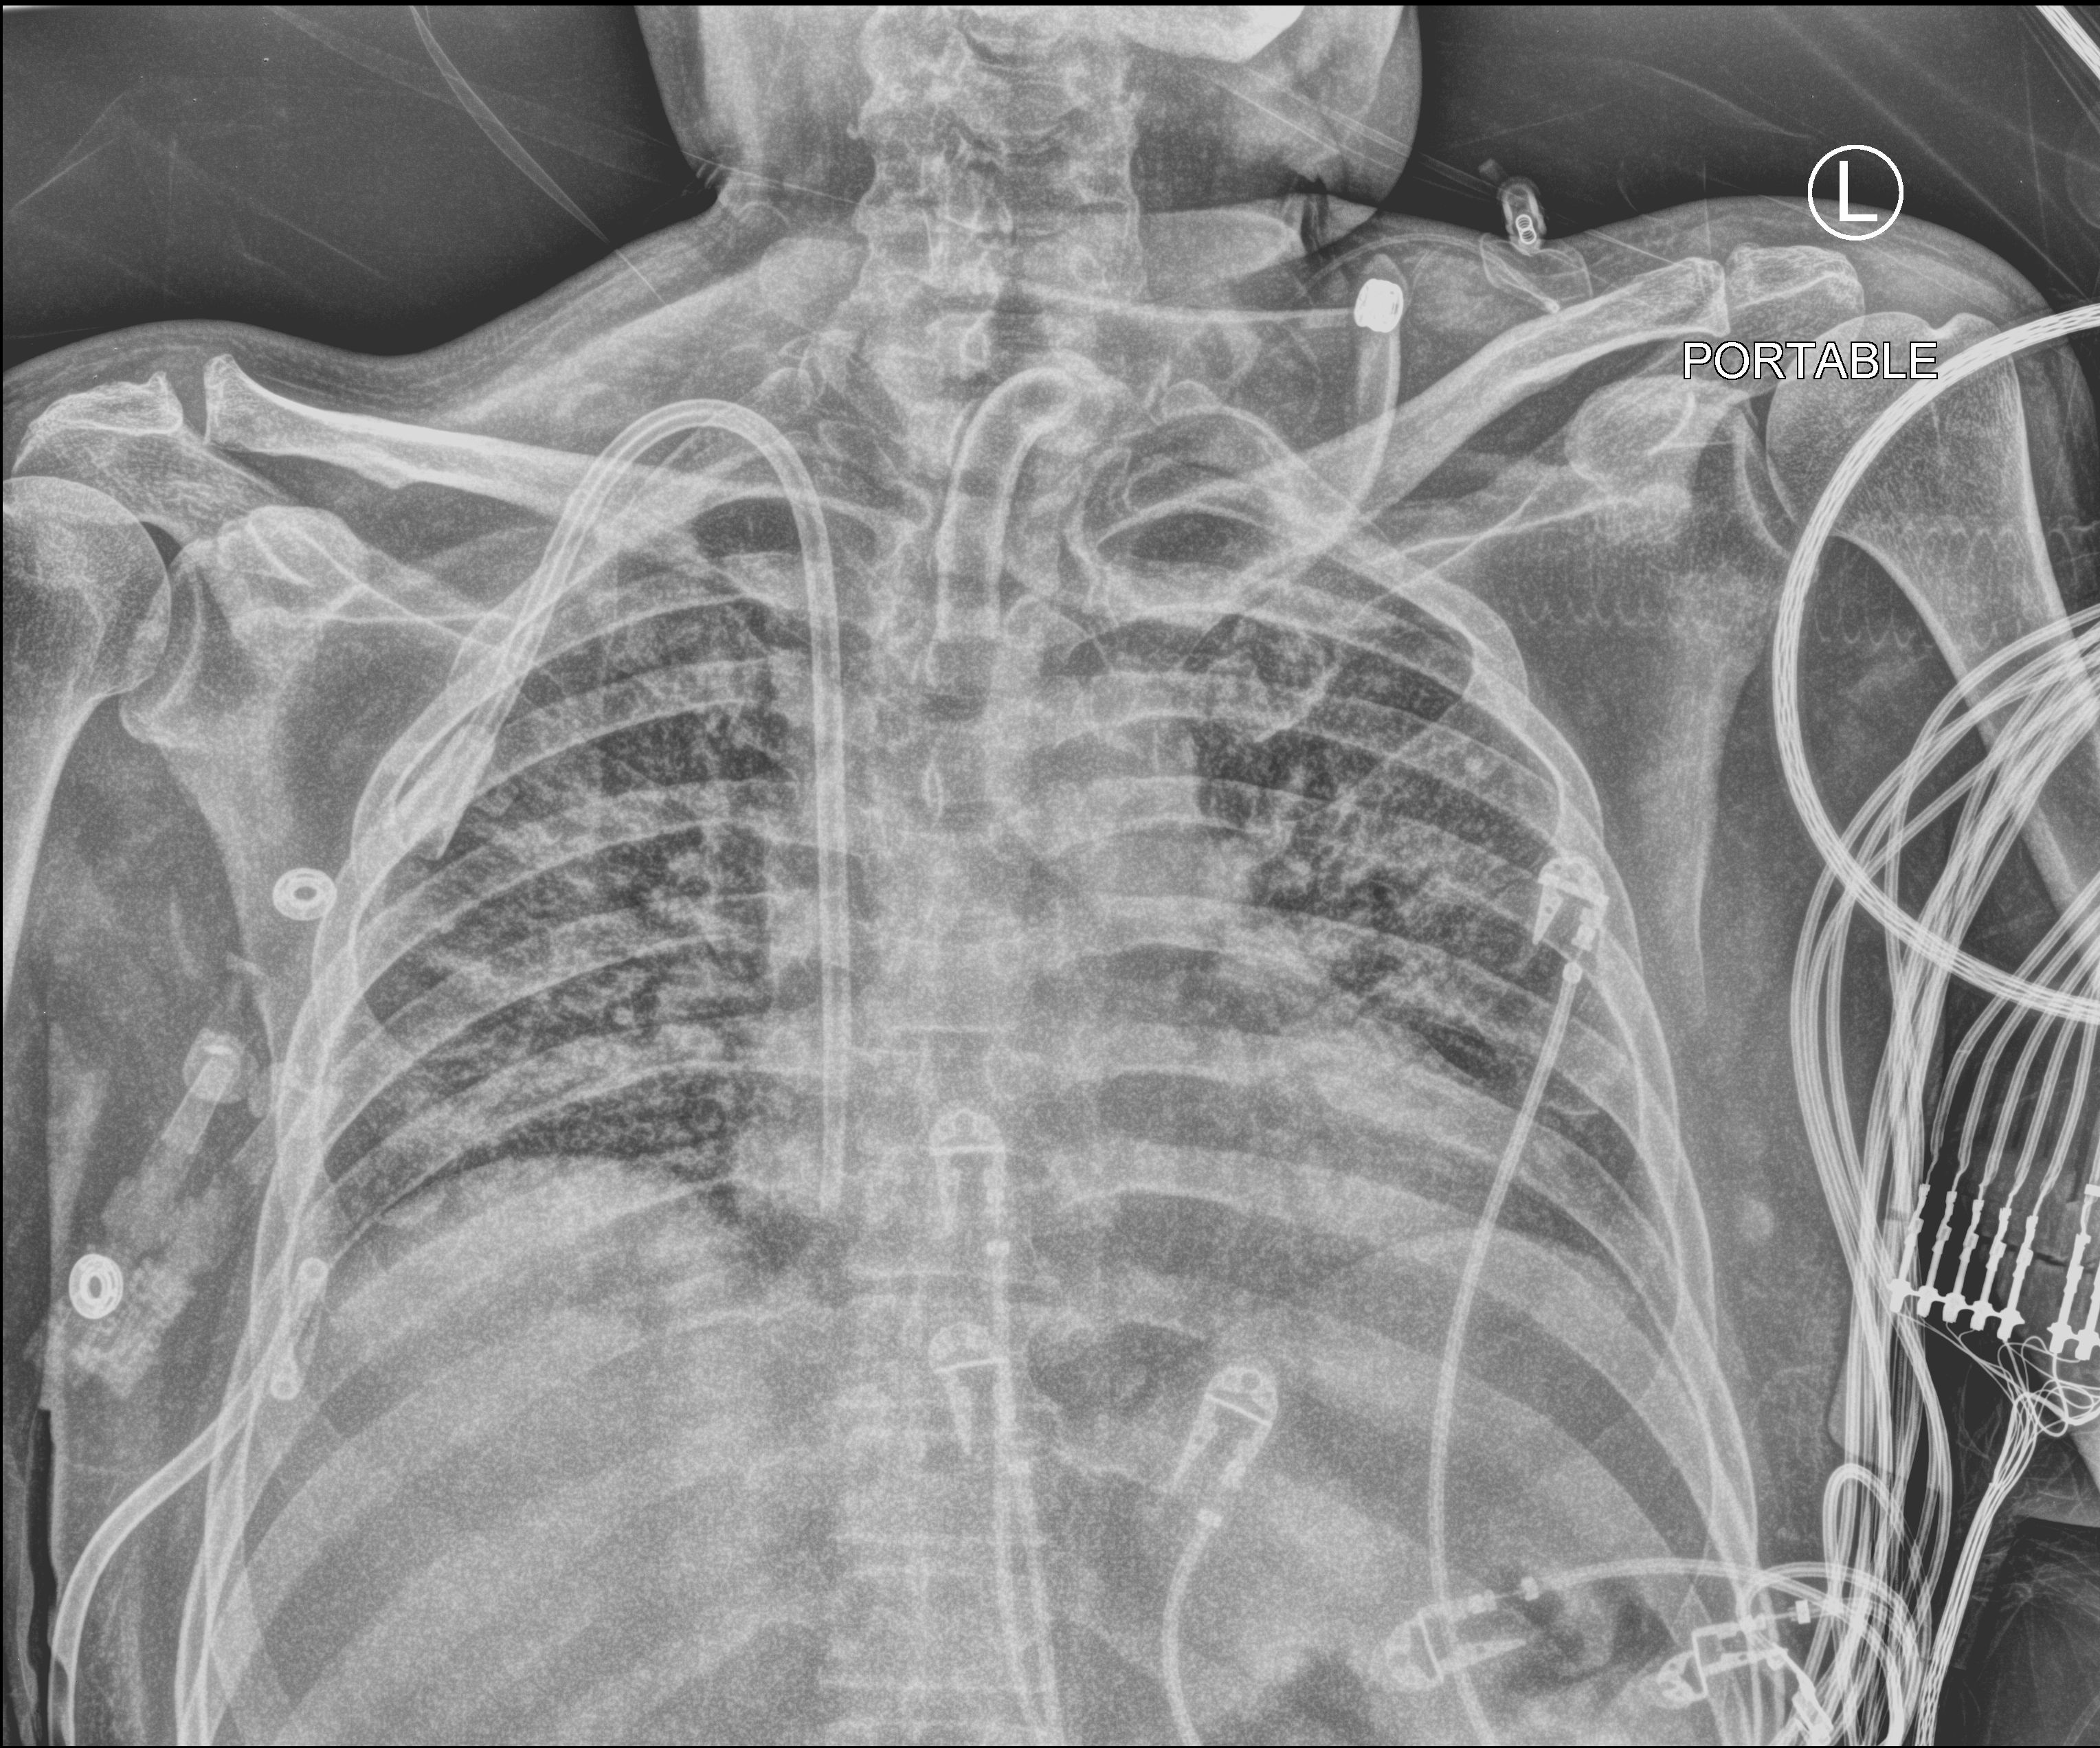
Bedside chest radiograph (computed radiography), anteroposterior (AP) projection. Male patient hospitalised with COVID-19, age 18–59 years.
Hospital-stay facts (about this admission, not read from this image; timing relative to this image not recorded): length of hospital stay: 77 days.